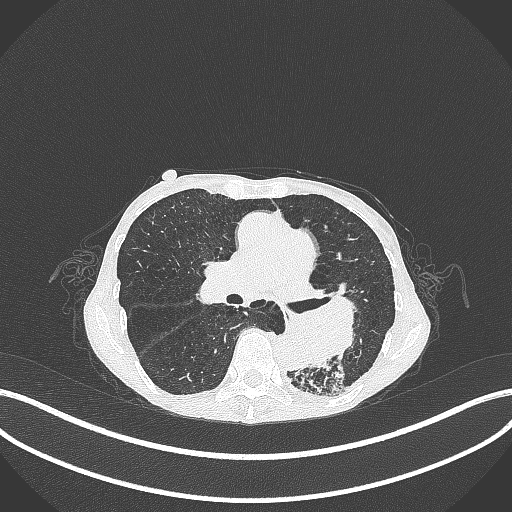
Chest CT, one axial slice. Slice 153 of 347 in the series (ordered by position). 120 kVp. Lung window (W 1500 / L -600 HU). 1 mm slice thickness. 512 × 512 image matrix, field of view 400 × 400 mm. Female patient, age 70 years. Case-level facts recorded for this patient, not image findings: clinical TNM (as recorded): T3 N0 M0.
Outlined on this slice (bounding box drawn by a radiologist):
- lung tumour (recorded histology: small cell carcinoma): bounding box (x1, y1, x2, y2) in pixels: (258, 292, 359, 382)